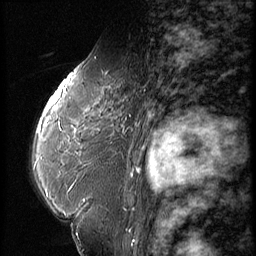
Breast MRI (dynamic contrast-enhanced), one sagittal slice. Position 37 of 56 along the scan axis. Dynamic contrast-enhanced series, image 2 of 3 at this slice position (ordered by acquisition). 1.5 T. TE 4.2 ms, TR 9 ms. 2.5 mm slice thickness. 256 × 256 image matrix, field of view 180 × 180 mm. Patient: female, 59 years. From the clinical record (not read from this slice): setting: breast cancer imaged before/during neoadjuvant chemotherapy; receptor status: HER2-positive.
Structures marked on this image (semi-automatic segmentation, software-assisted and operator-edited):
- analysis volume of interest (the breast-tissue region the enhancement analysis was run in; not a lesion): bounding box (x1, y1, x2, y2) in pixels: (44, 66, 151, 135)
- tumour enhancement mask (voxels above the 140 % enhancement threshold inside the analysis volume of interest): (46, 75, 70, 111)